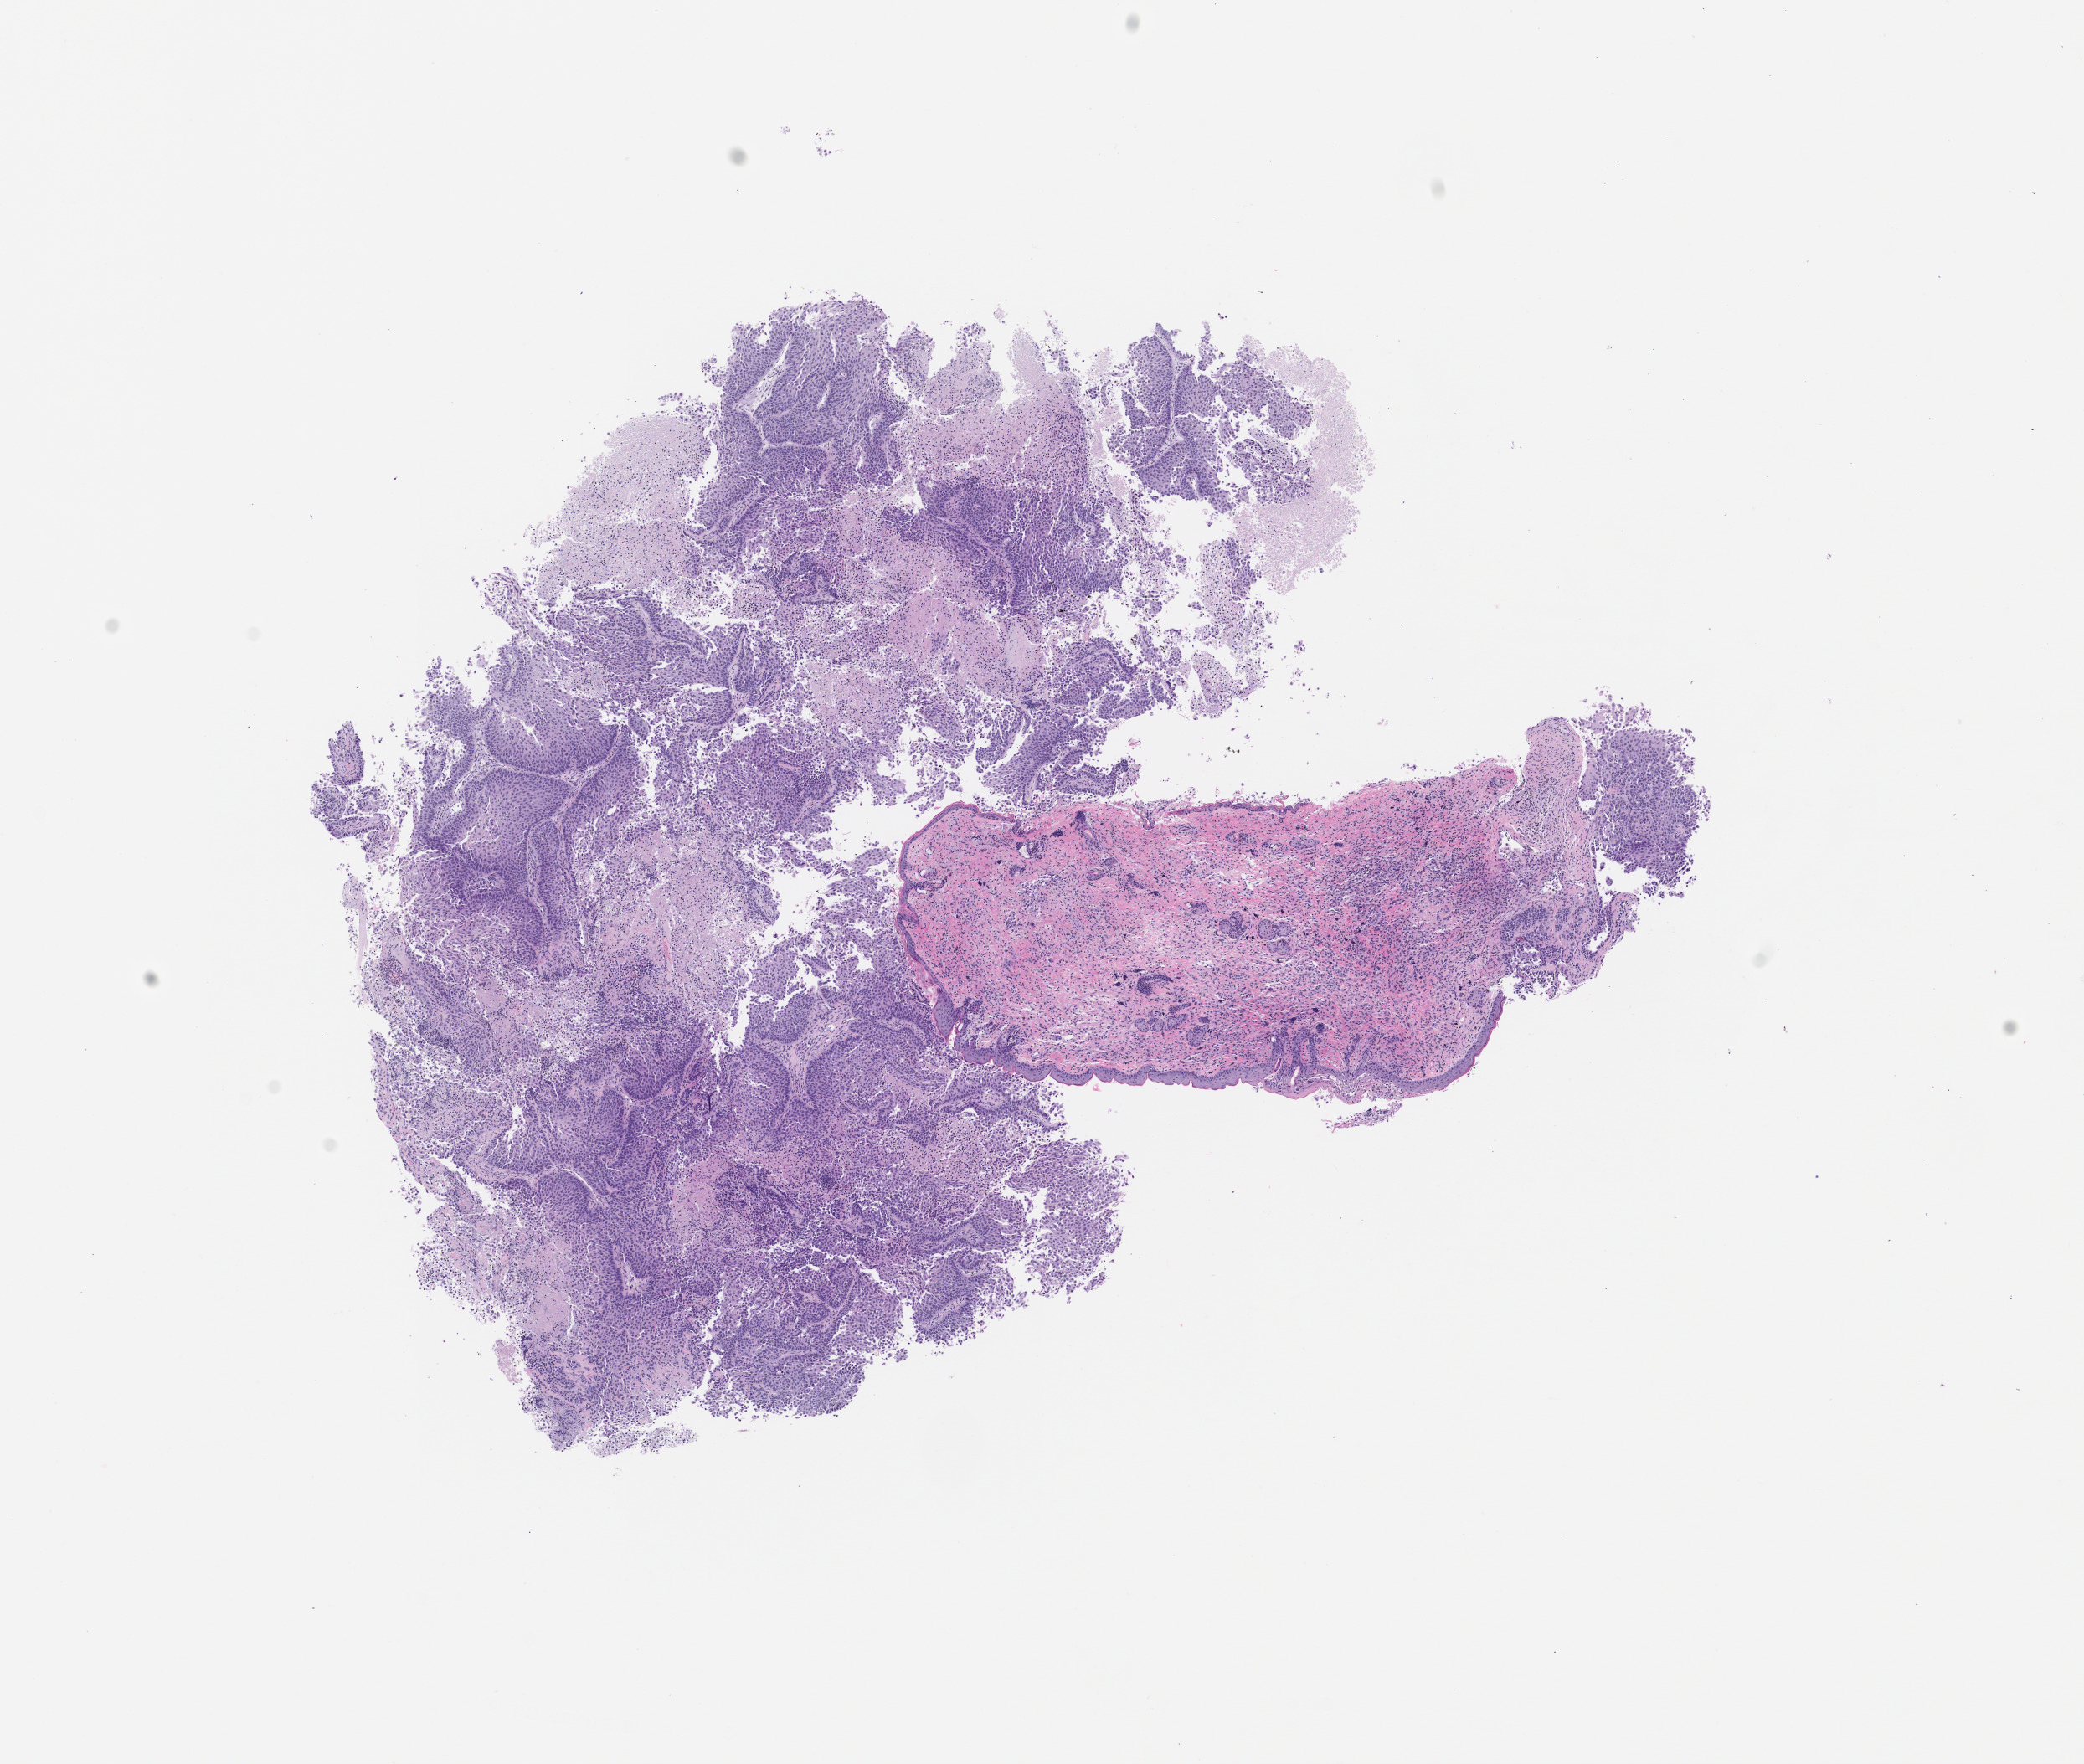
H&E whole-slide image of a patient-derived xenograft (PDX) tumor grown in a mouse, passage 2, whole scanned area (about 10.0 x 8.4 mm) shown as a low-resolution overview, FFPE section, tumor site category: bladder.
• originating patient diagnosis: Urothelial Carcinoma